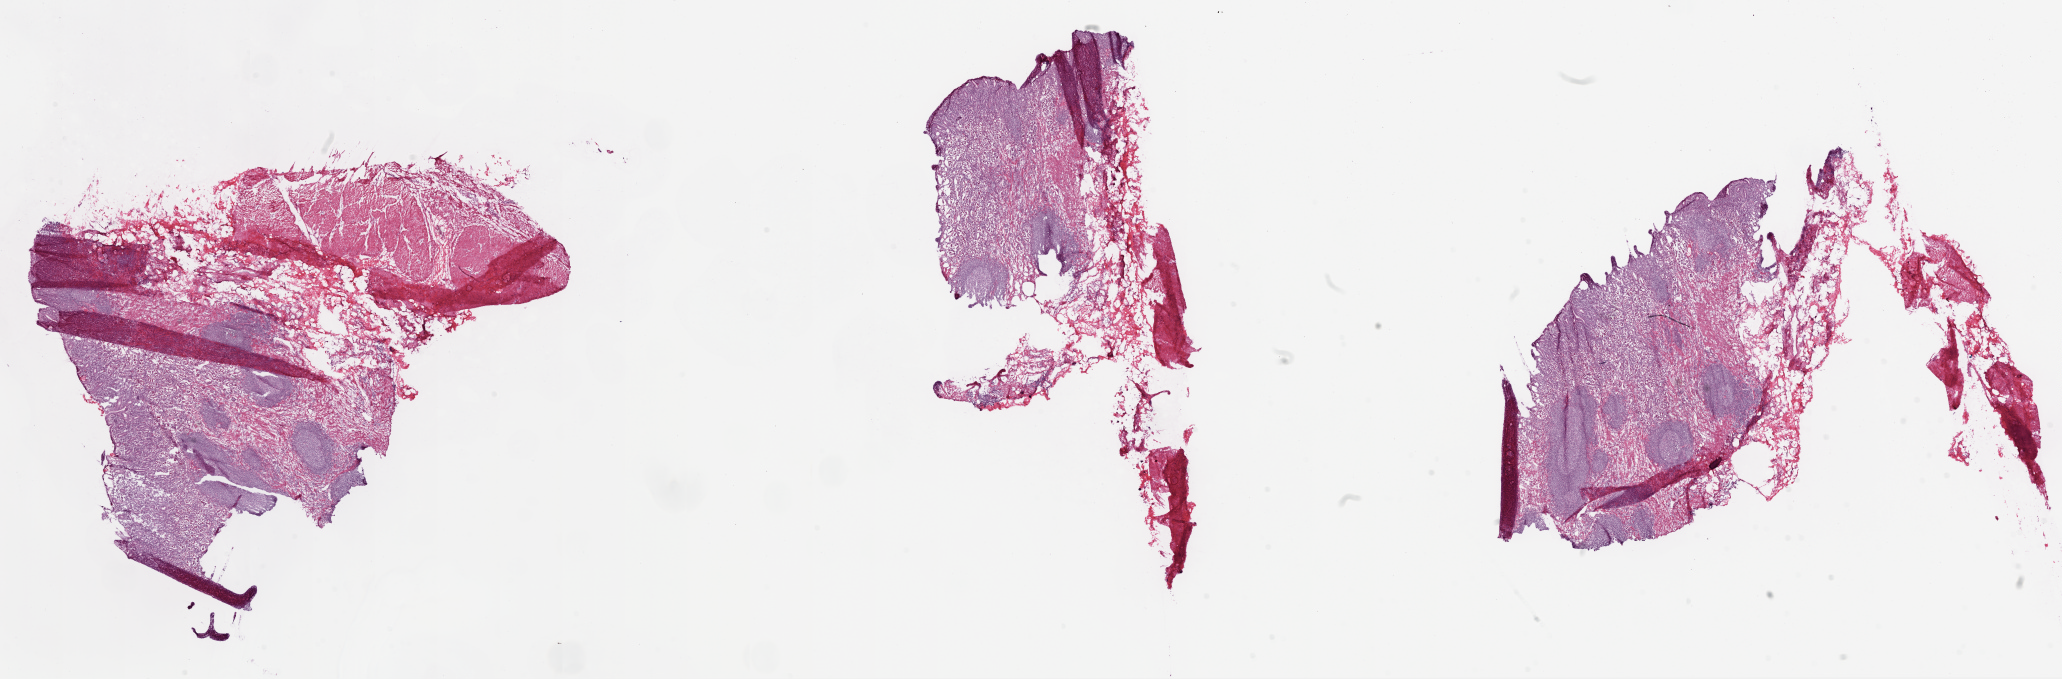
Digitized H&E-stained tissue section (whole slide), shown as a low-resolution overview of the whole scanned area (about 33.1 x 10.9 mm, slide scanned at 20x), frozen section, solid tissue normal (non-tumour tissue) sample from the stomach. Male, age 51 years at initial diagnosis.
- this section: solid tissue normal sample (biorepository sample class)
- patient diagnosis: Adenocarcinoma, NOS (body of stomach)